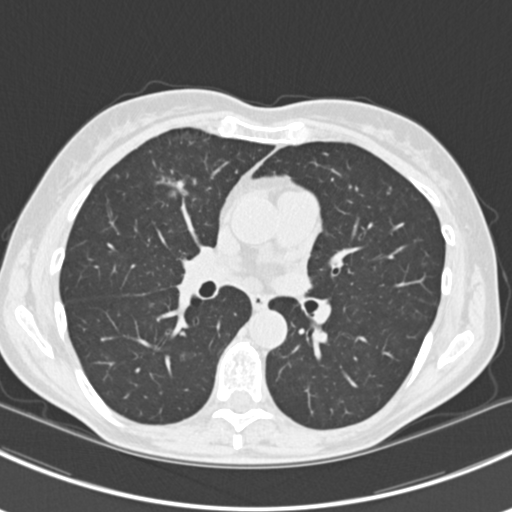
Chest CT (low-dose screening protocol), one axial image. Baseline annual screen. Lung window (W 1500 / L -600 HU). Slice 86 of 224 in the series. 512 × 512 image matrix. Female participant, aged 63 years at enrolment.
Expert reader's lesion annotation, bounding box (x1, y1, x2, y2) in pixels: (143, 160, 204, 217). The screening reader recorded 10 non-calcified nodules or masses ≥4 mm on this exam (right lower lobe, right lower lobe, left lower lobe, left lower lobe, right middle lobe, right lower lobe, left lower lobe, left upper lobe, right upper lobe, left upper lobe); which of them this box marks is not recorded. Official screen result: positive, change unspecified: nodule(s) >= 4 mm or enlarging nodule(s), mass(es), or other non-specific abnormalities suspicious for lung cancer. Lung cancer was diagnosed 751 days after this screen: bronchiolo-alveolar adenocarcinoma, NOS, right upper lobe, right middle lobe, right lower lobe, left upper lobe, left lower lobe, moderately differentiated (G2), stage IV (AJCC 6th edition).